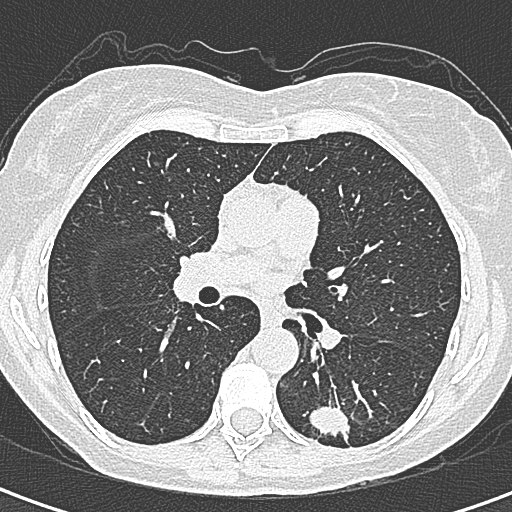
Chest CT (low-dose screening protocol), one axial image, baseline annual screen, lung window (W 1500 / L -600 HU), 1 mm slice thickness, 512 × 512 image matrix. Female, age 58 years at enrolment. Former smoker at enrolment.
Expert-annotated lung lesion, box from (x=298, y=386) to (x=367, y=456) px. The screening reader recorded 2 non-calcified nodules or masses ≥4 mm on this exam (left lower lobe, right lower lobe); which of them this box marks is not recorded. Participant outcome: lung cancer diagnosed 22 days after this screen — adenocarcinoma, NOS, left lower lobe, moderately differentiated (G2), stage IA (AJCC 6th edition), 25 mm at pathology.